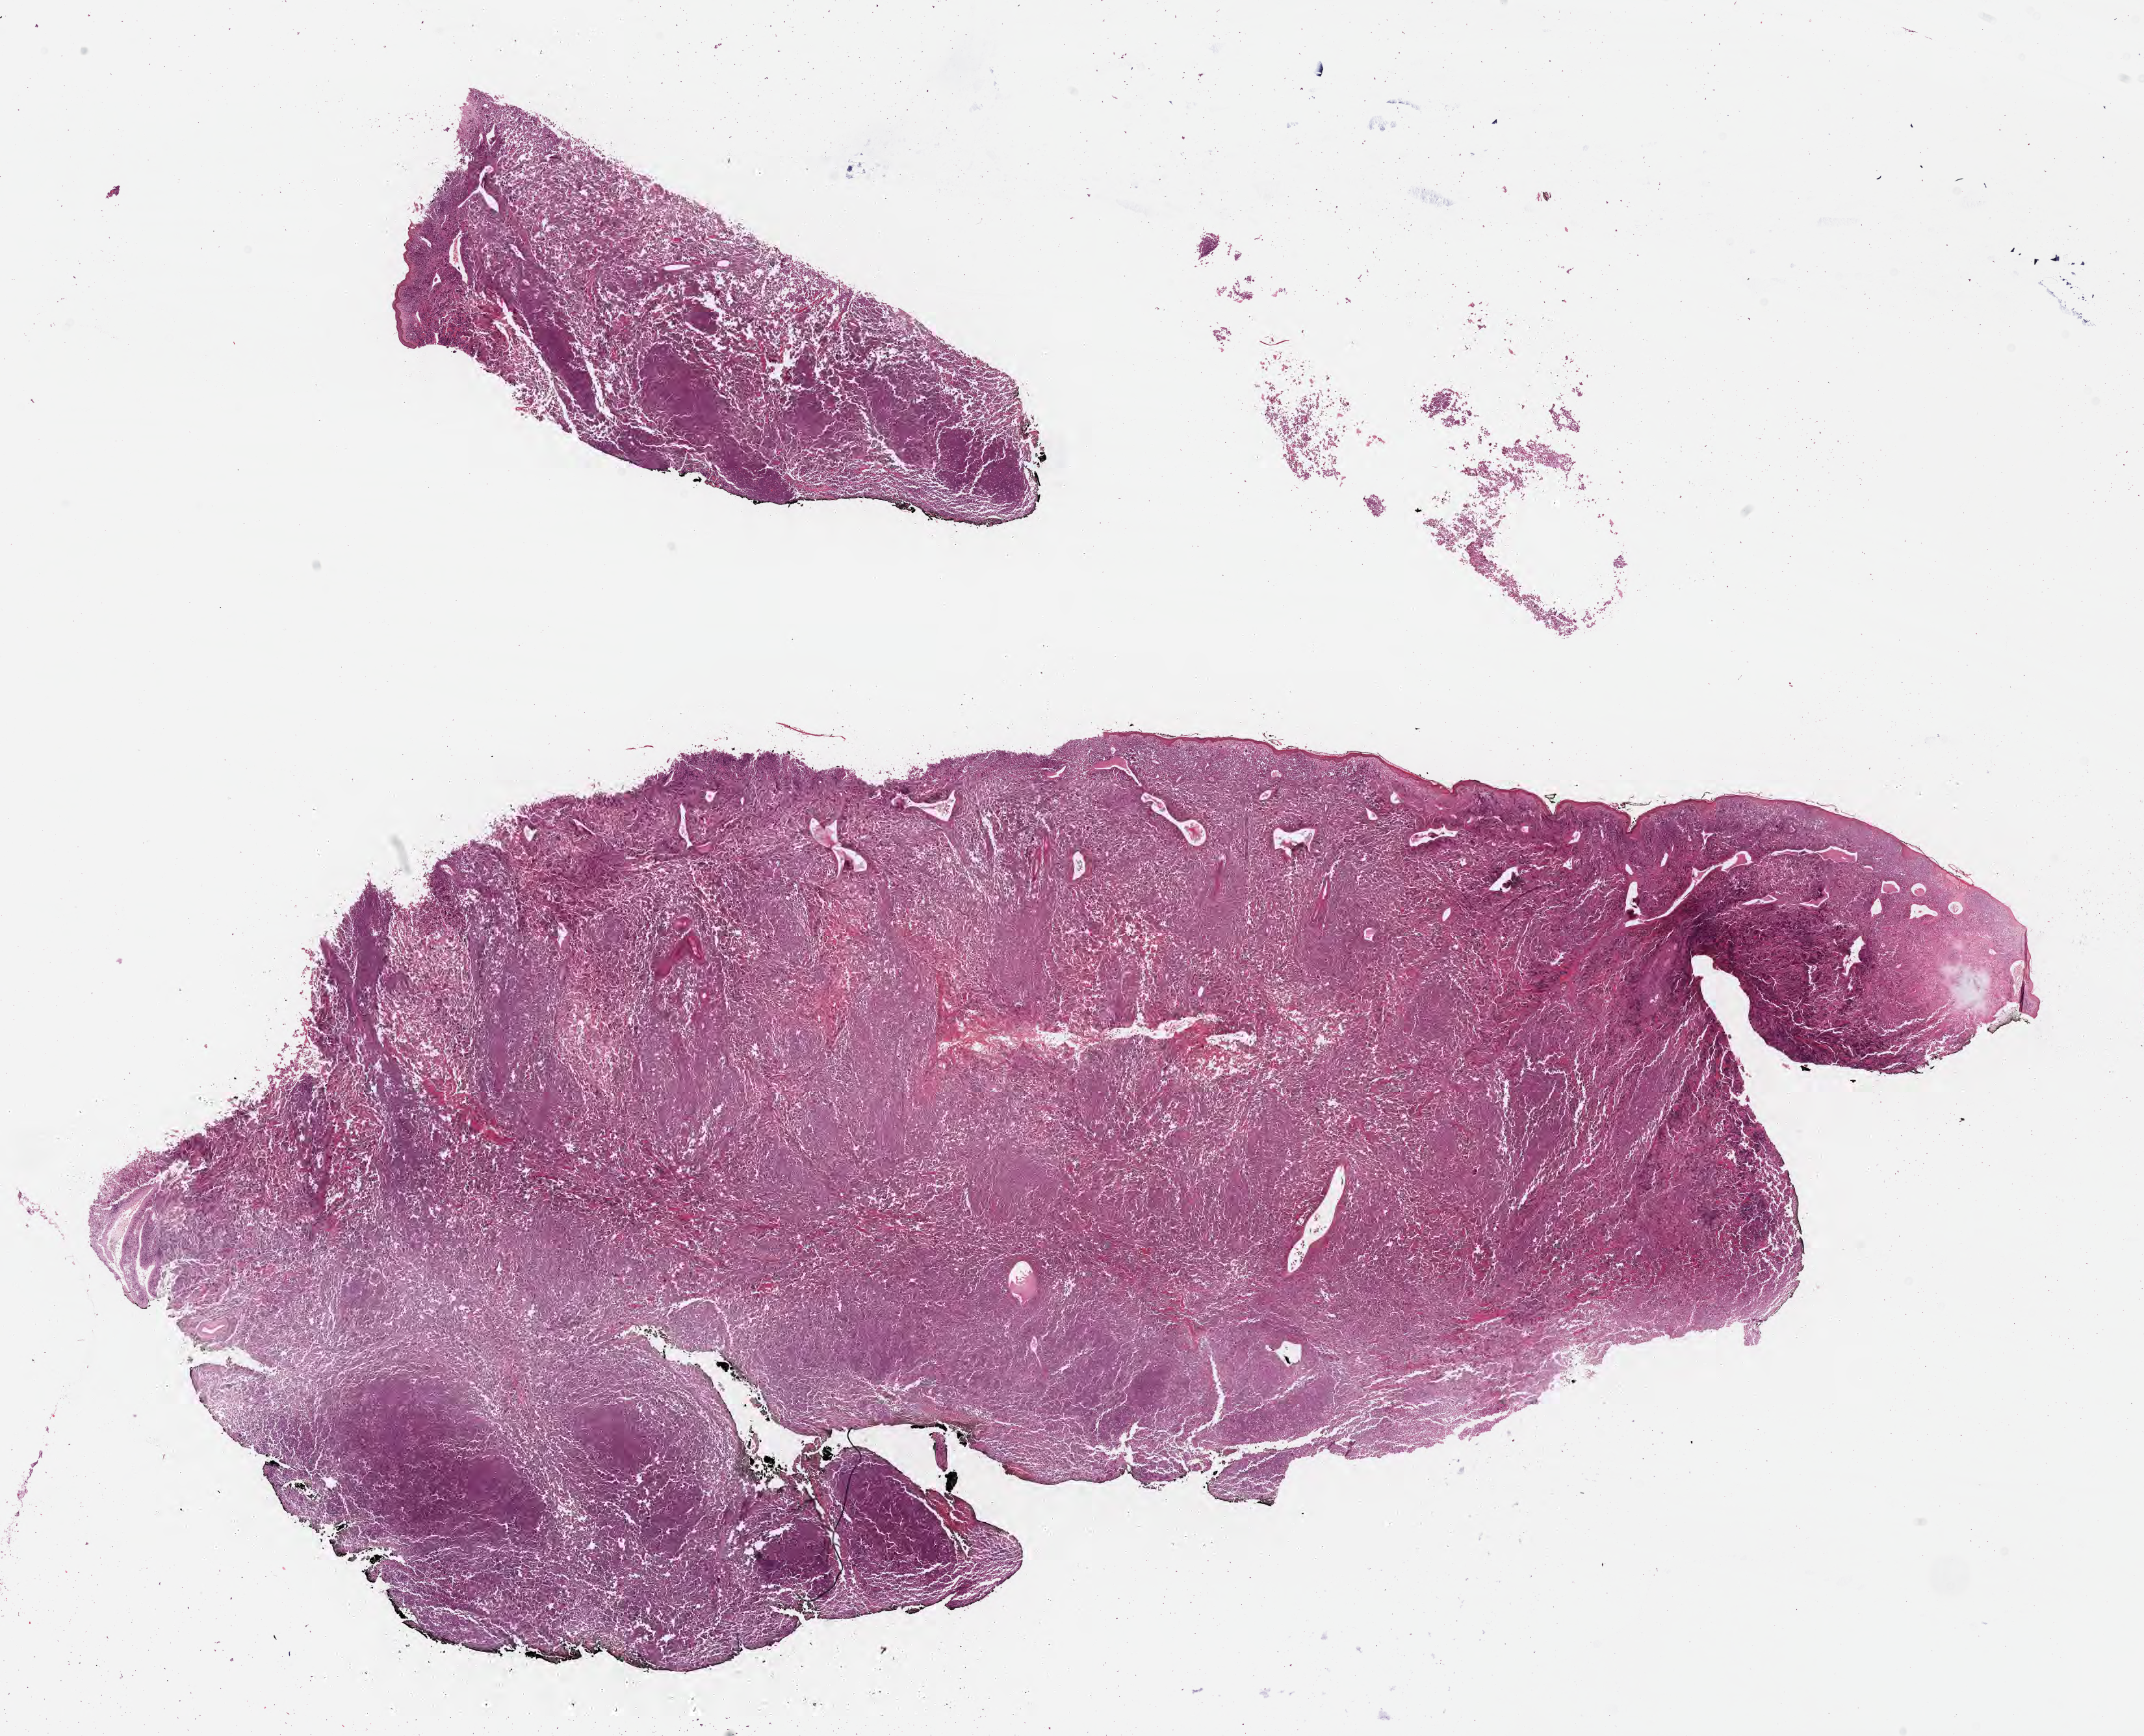
Whole-slide image, haematoxylin and eosin stain — whole scanned area (about 26.7 x 21.6 mm) shown as a low-resolution overview. Formalin-fixed paraffin-embedded section. Specimen: primary tumor. Patient male; 46 years old. Slide review estimates, as recorded: tumor cells 90%, tumor nuclei 95%, stromal cells 10%, necrosis 0%, normal cells 0%. Infiltration values recorded for this section: lymphocyte infiltration 70%, monocyte infiltration 15%, neutrophil infiltration 5%.
Histologic diagnosis: Burkitt lymphoma, NOS. Ann Arbor stage (patient): Stage III. Section: top of the tissue portion.